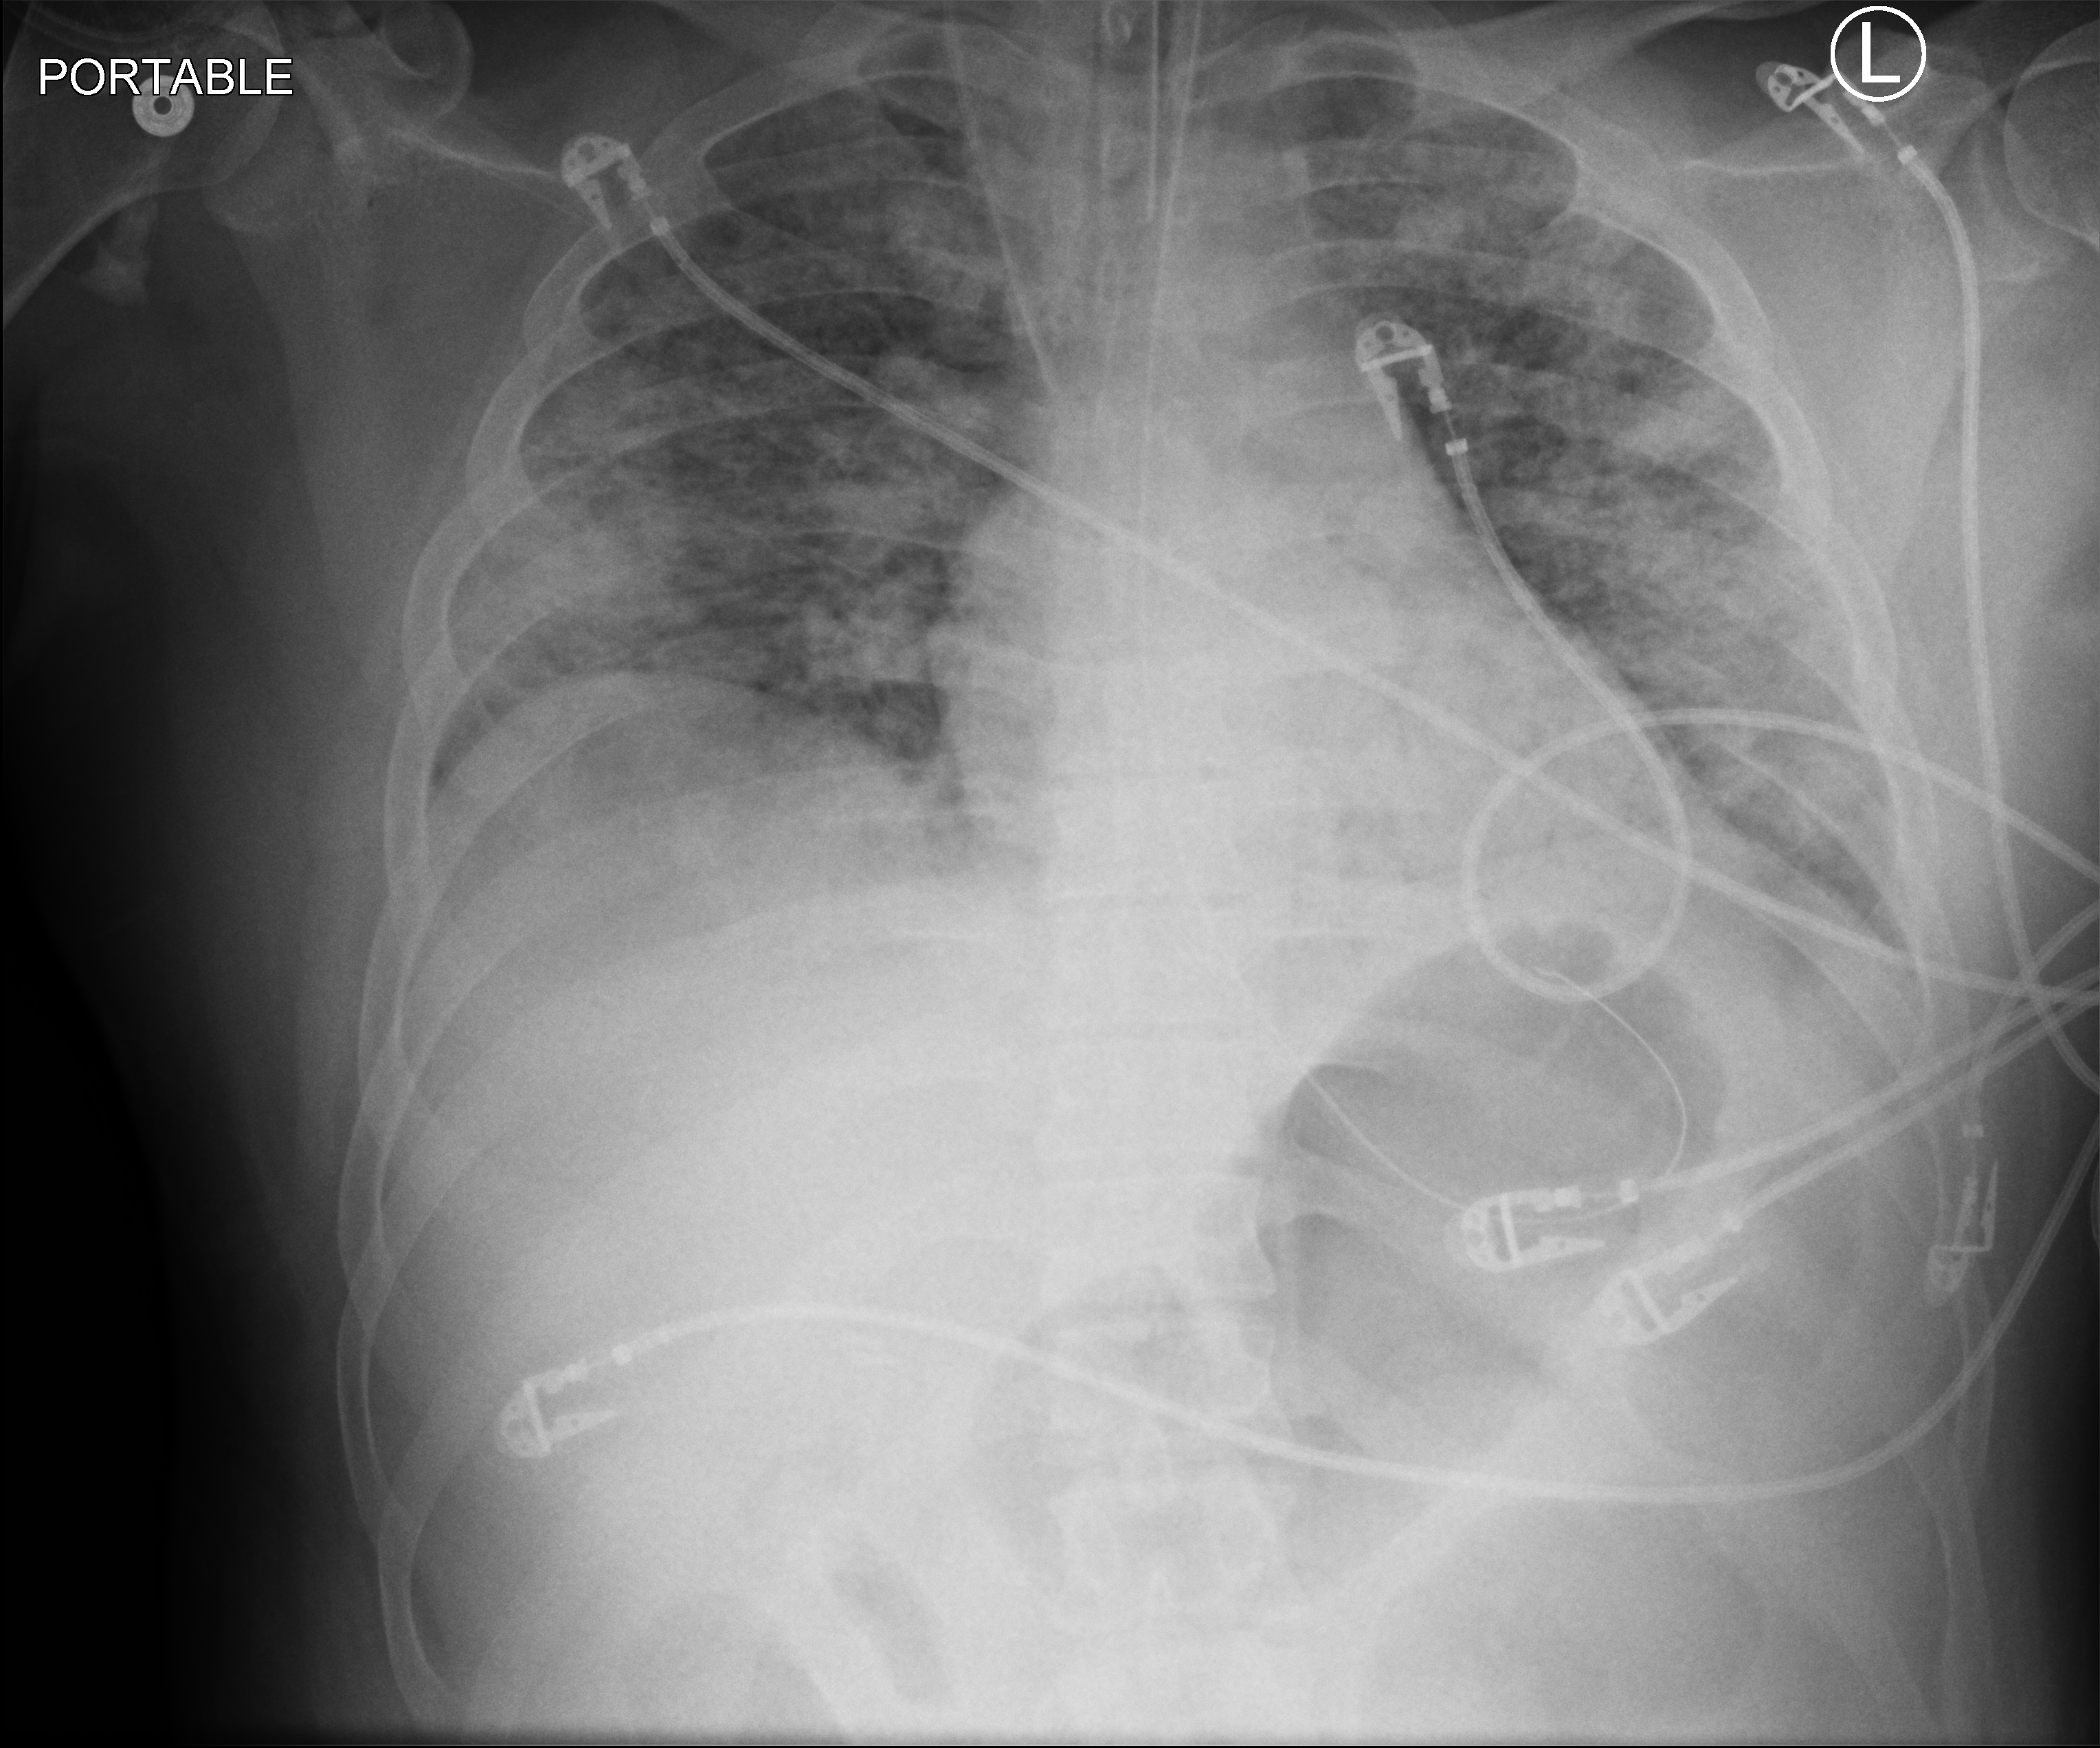
Chest X-ray (portable). Male patient hospitalised with COVID-19, age 18–59 years.
Hospital-stay facts (about this admission, not read from this image; timing relative to this image not recorded):
- length of hospital stay: 44 days